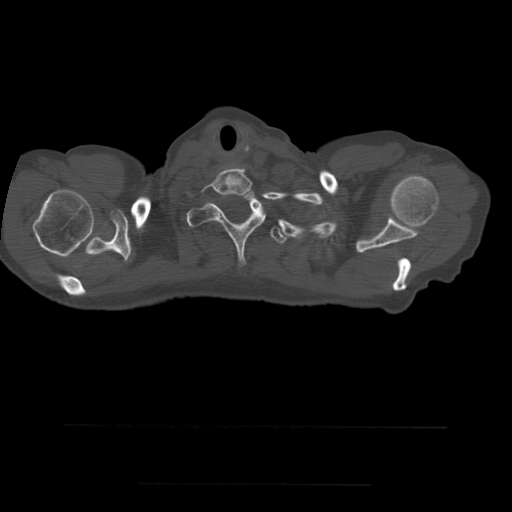
CT including the spine, one axial slice; slice 447 of 544 in the series (ordered by position); bone window (W 1800 / L 400 HU); 1.25 mm slice thickness; 512 × 512 image matrix. Patient age 58 years. Case-level facts recorded for this patient, not image findings: primary cancer: lung.
Structures marked on this image (semi-automatic segmentation, software-assisted and operator-edited):
- T1 vertebra: bounding box <187,191,266,264> (left, top, right, bottom; pixels)
- T2 vertebra: <270,226,289,244>